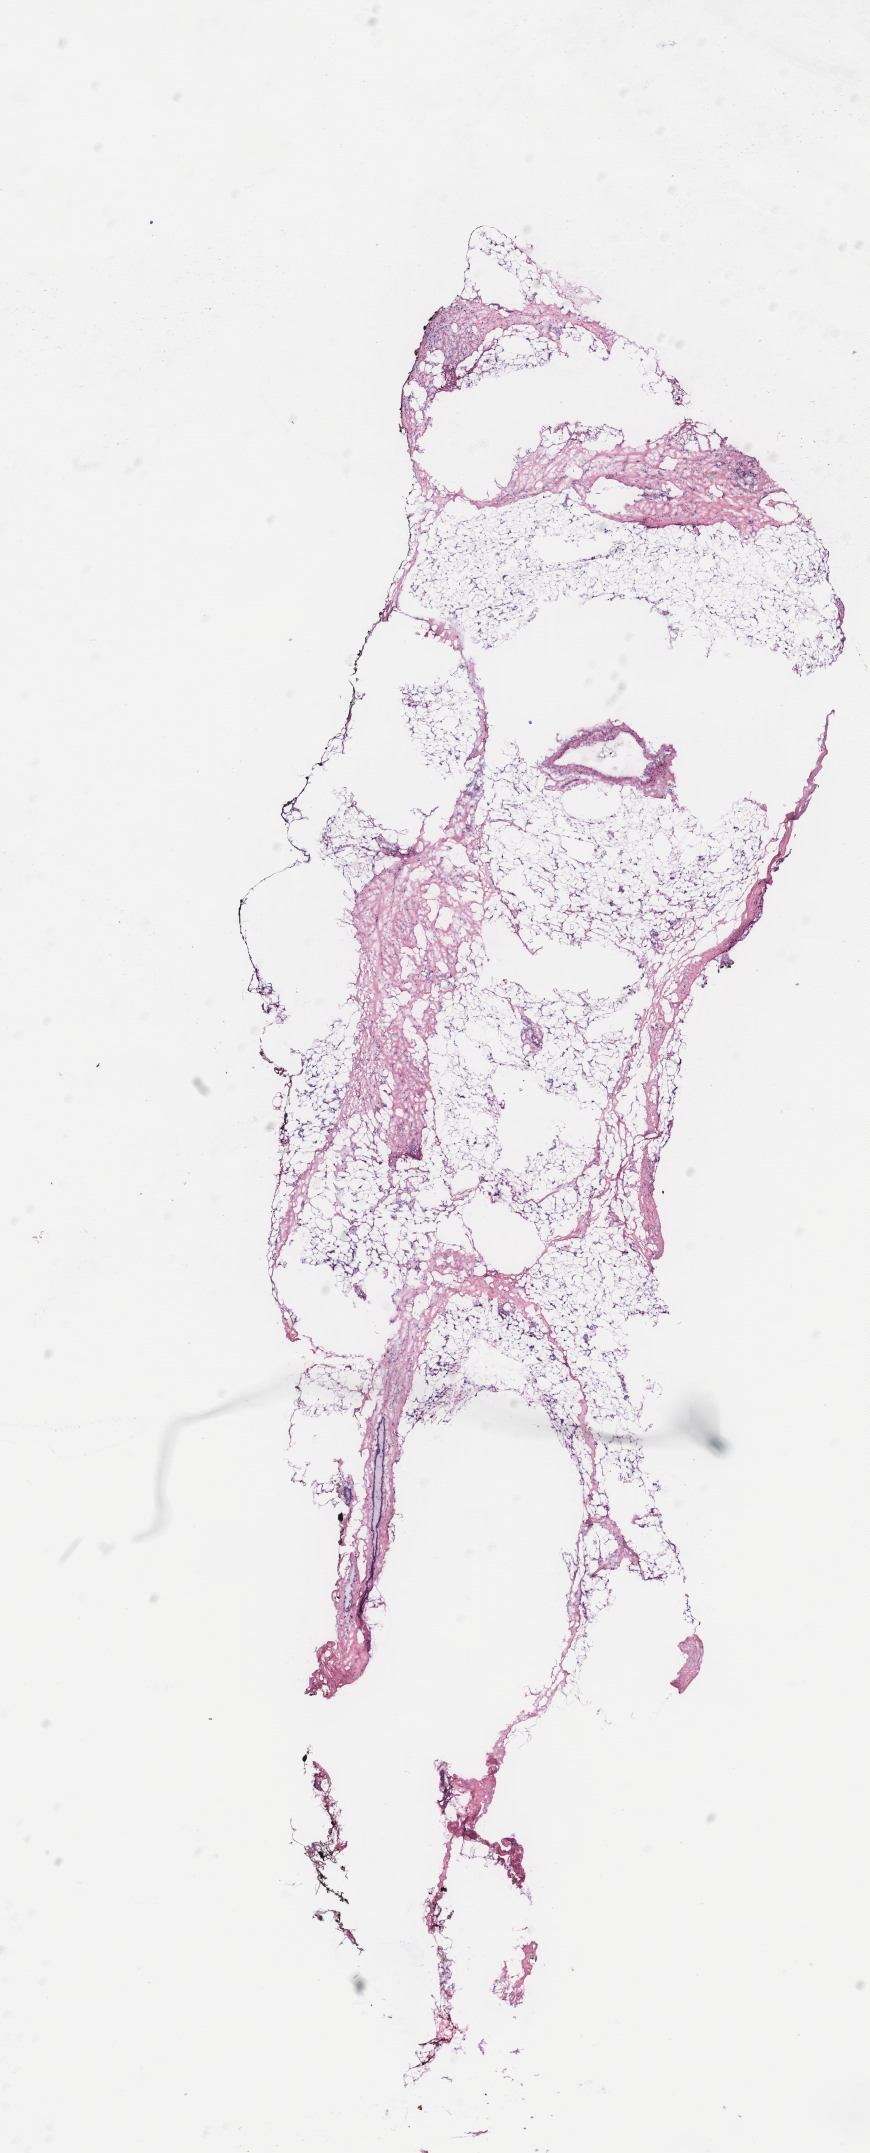
Whole-slide histology image, H&E — low-resolution overview of the scanned area, about 7.0 x 17.2 mm. Tumour tissue sample, breast. Patient: female, age 61 years.
• AJCC pathologic stage: IIA
• diagnosis: Infiltrating lobular carcinoma, NOS